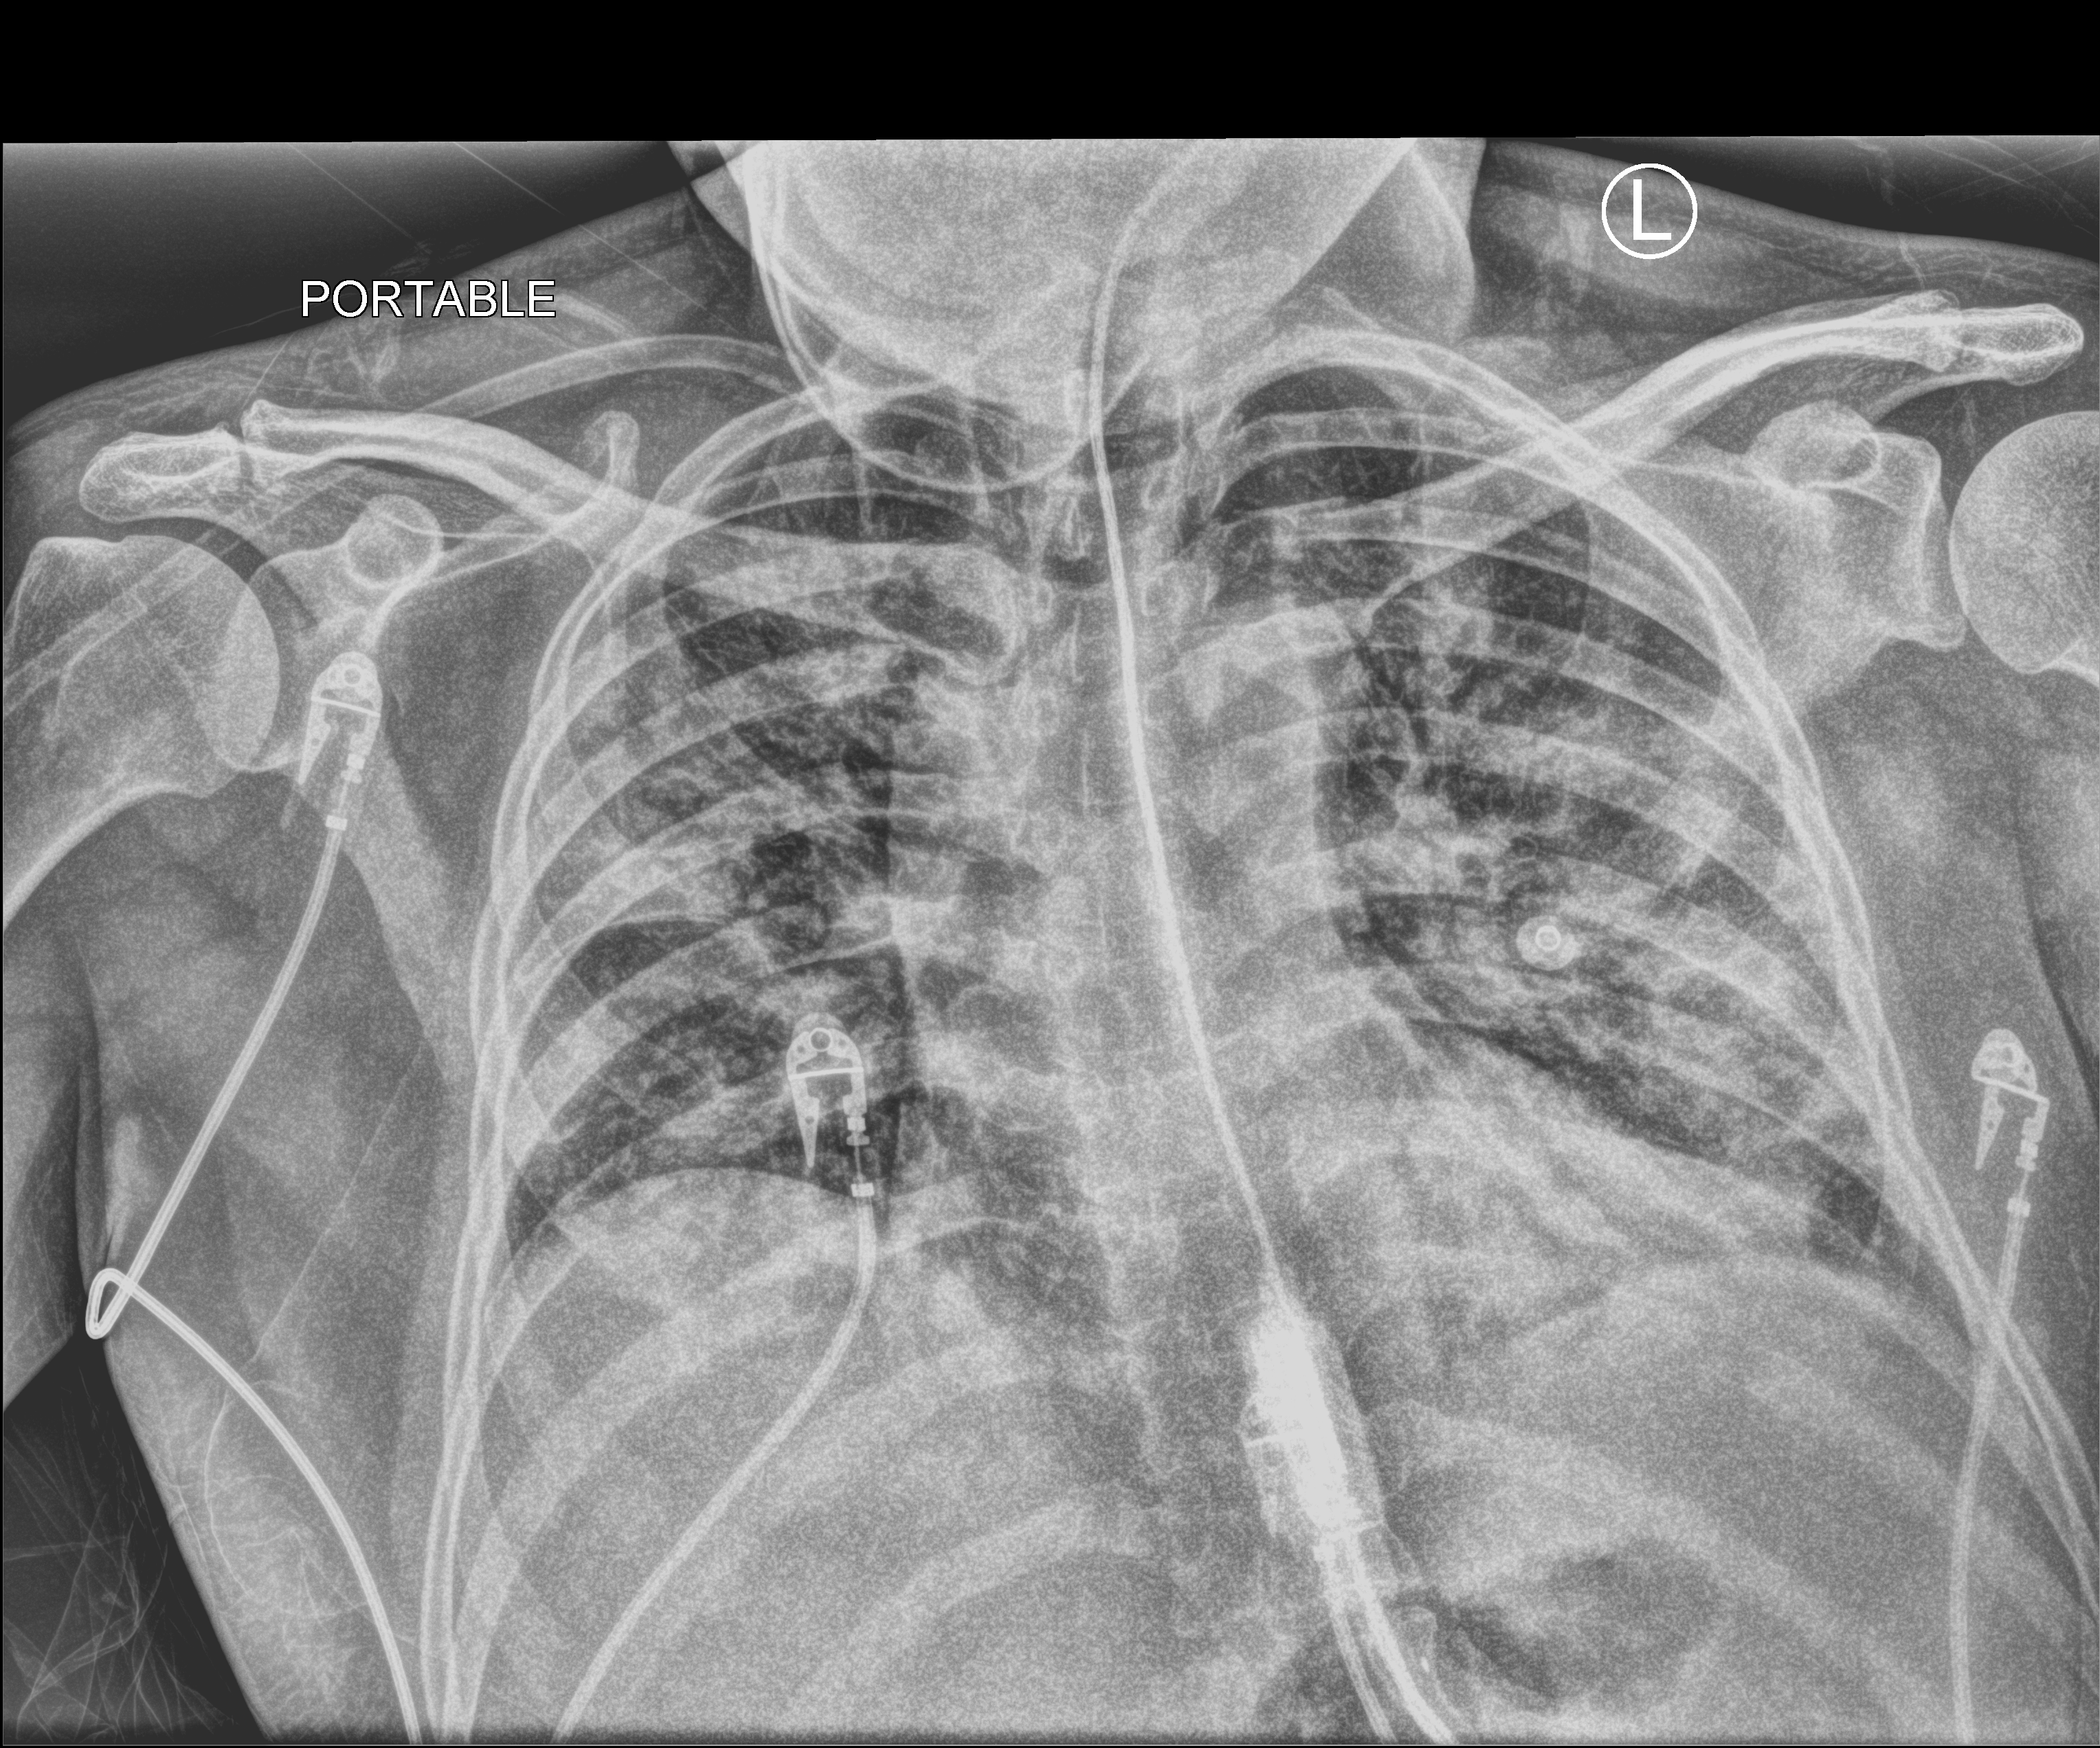
Bedside chest radiograph (computed radiography), anteroposterior (AP) projection. Male patient hospitalised with COVID-19, age 18–59 years.
From the hospital-stay record, not from the radiograph (when in the stay this image was taken is not recorded):
- COPD (admission record): no
- admitted to intensive care during this hospital stay: yes